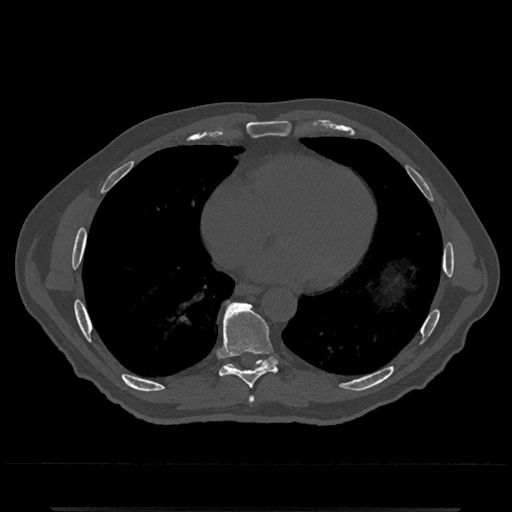
CT including the spine, one axial slice. Position 659 of 797 along the scan axis. Reconstruction kernel Br40s/3. 120 kVp. Bone window (W 1800 / L 400 HU). 0.5 mm slice thickness. 512 × 512 image matrix, field of view 393 × 393 mm. Male patient, age 67 years. From the clinical record (not read from this slice): primary cancer: prostate.
Outlined on this slice (semi-automatically segmented with operator editing):
- T7 vertebra: box from (x=248, y=396) to (x=254, y=404) px
- T8 vertebra: (x=217, y=300)–(x=278, y=389)
- T9 vertebra: (x=219, y=303)–(x=277, y=369)